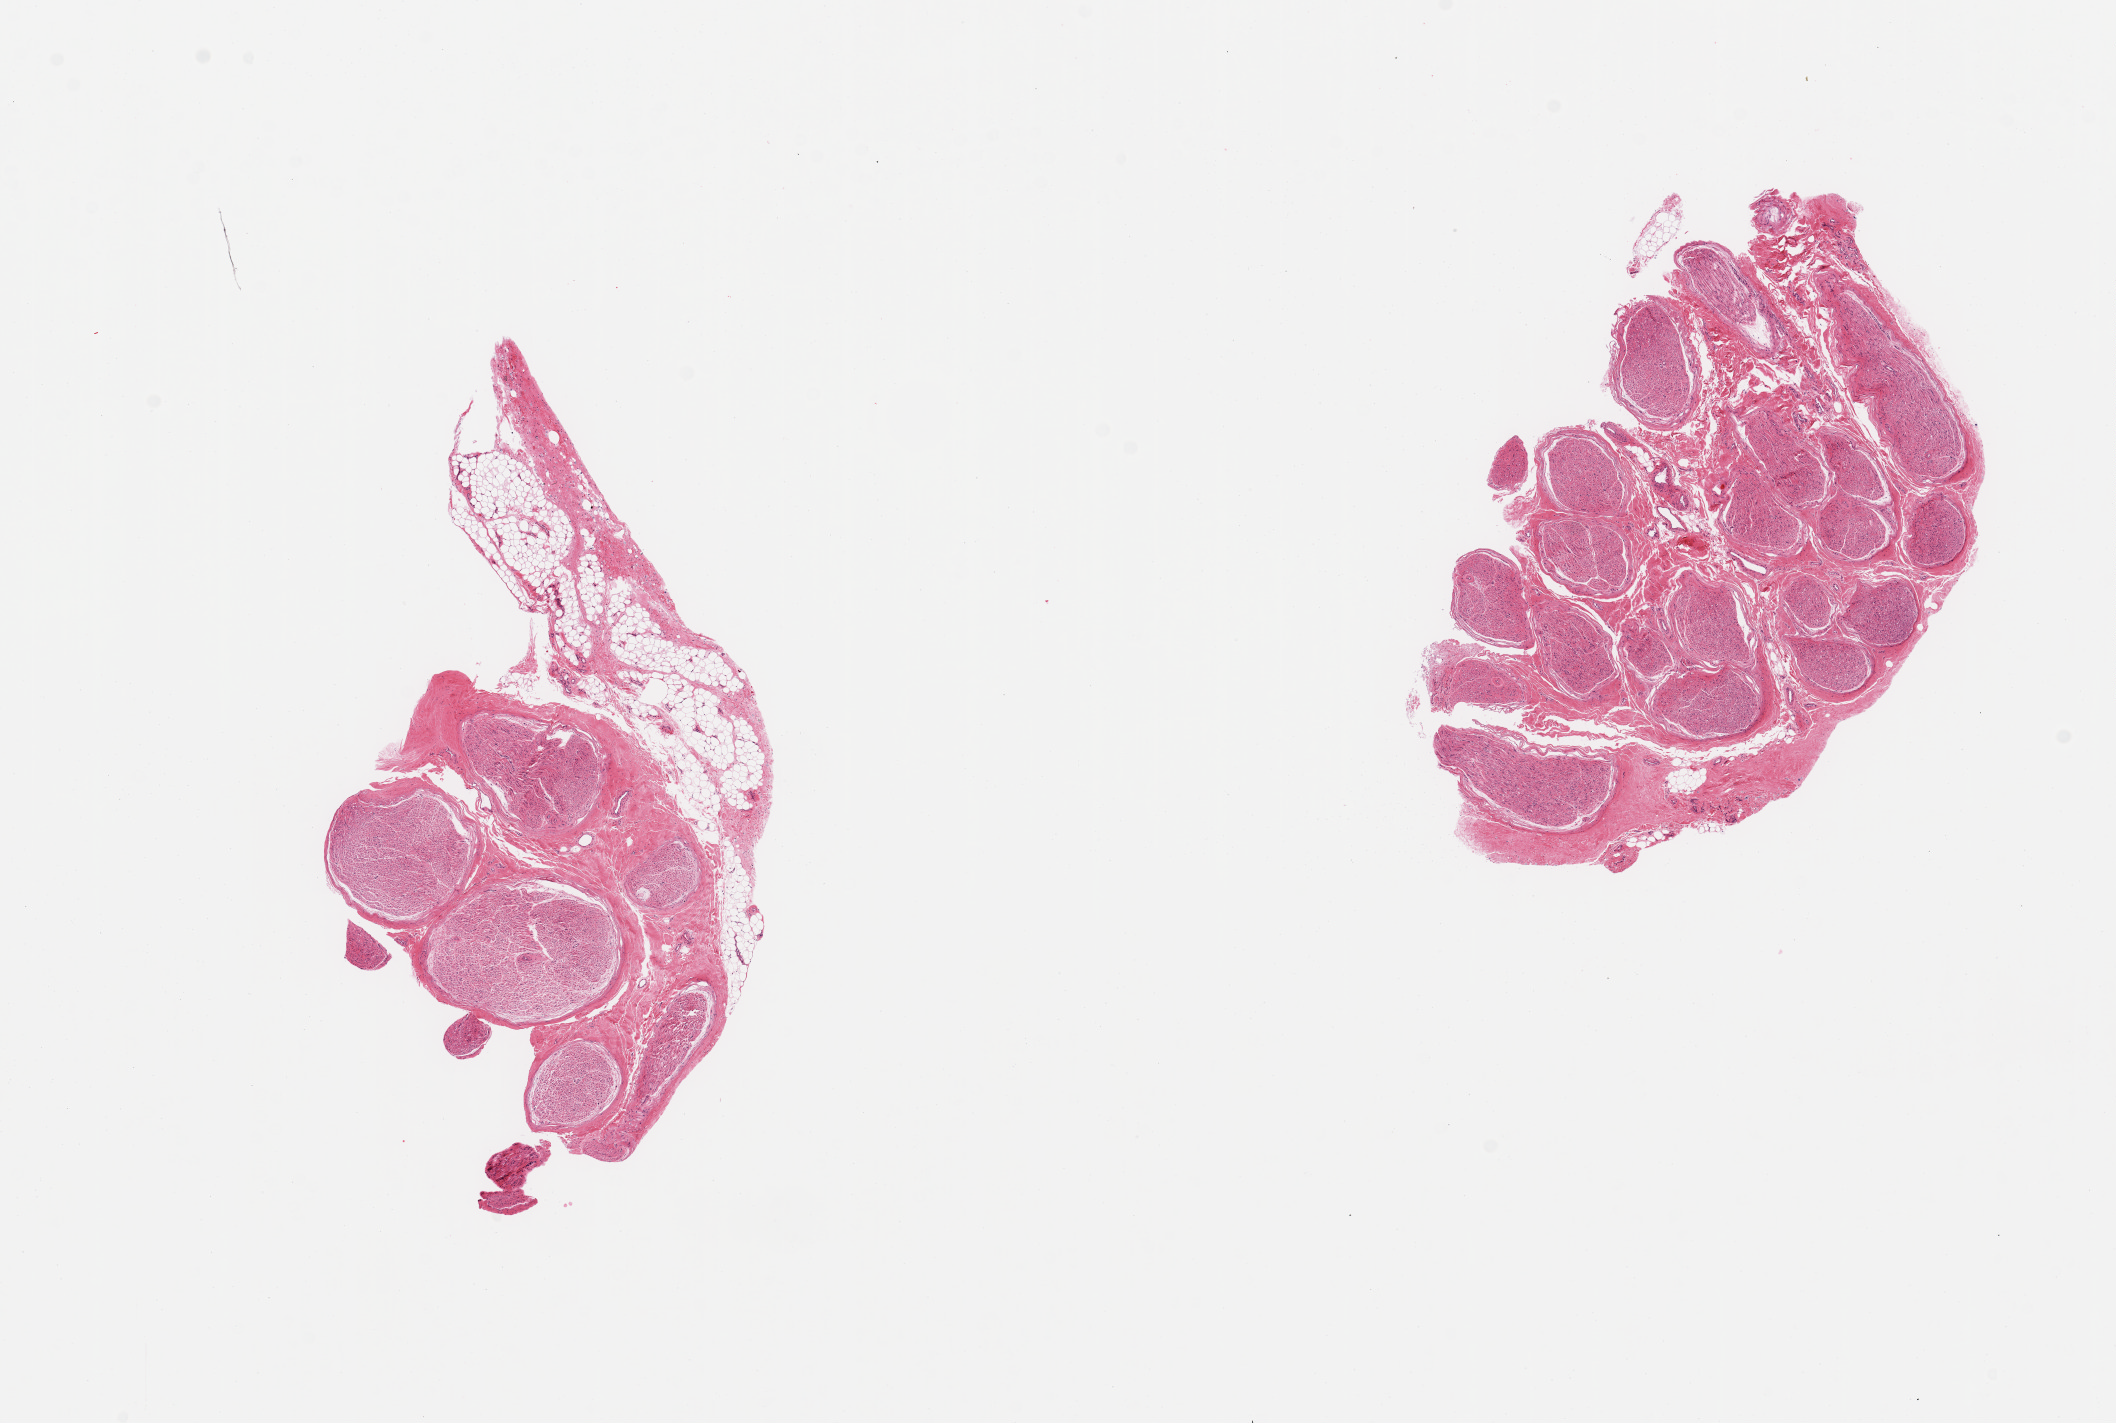
Digitized H&E-stained section, brightfield — a low-resolution overview of the entire scanned area, about 16.7 x 11.3 mm (acquisition: 20x scan); PAXgene-fixed, paraffin-embedded tissue; sampled site (target tissue): tibial nerve; donor tissue sample. Donor sex: male.
- pathologist's review note for this sample: 2 pieces, adherent nubbin of fibroadipose tissue, ~4x1mm